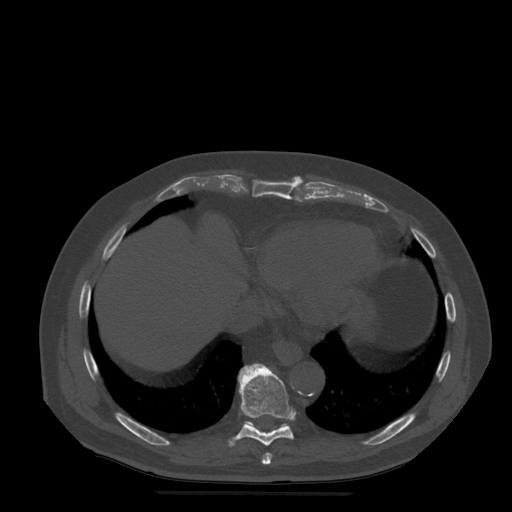
CT including the spine, one axial slice. Position 287 of 522 along the scan axis. Bone window (W 1800 / L 400 HU). 1.25 mm slice thickness. 512 × 512 image matrix, field of view 420 × 420 mm. Patient age 72 years. From the clinical record (not read from this slice): primary cancer: prostate.
Annotated regions visible in this slice (semi-automatically segmented with operator editing):
- T10 vertebra: box from (x=280, y=424) to (x=288, y=428) px
- T8 vertebra: (x=262, y=453)–(x=273, y=465)
- T9 vertebra: (x=229, y=363)–(x=294, y=447)